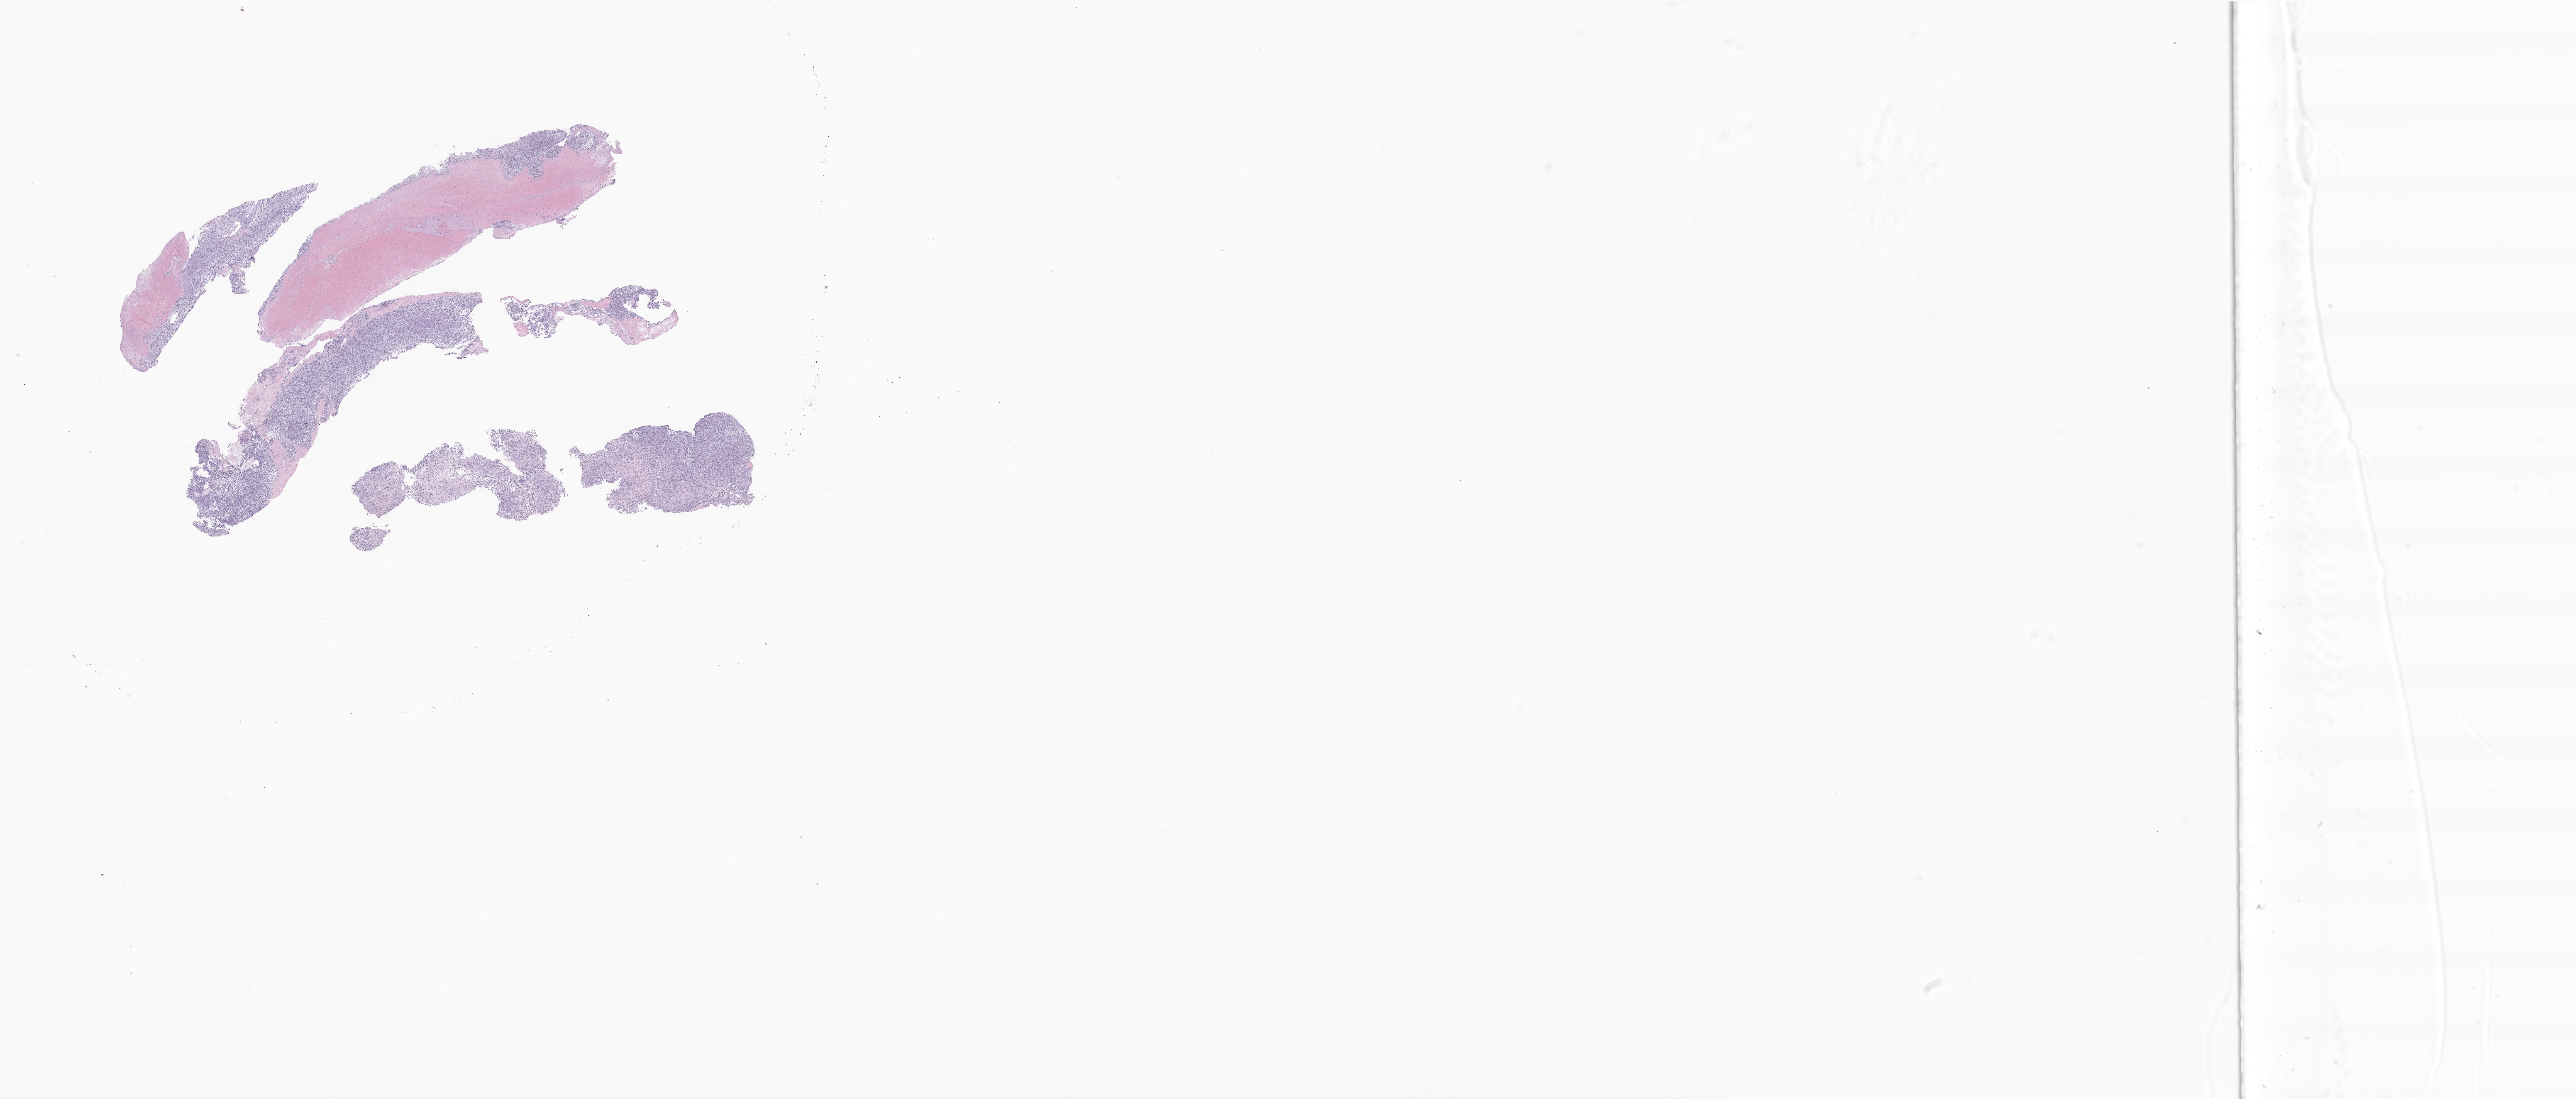
Whole-slide image, H&E stain of tumor tissue from the soft tissue of pelvis, low-resolution overview of the scanned area, about 39.0 x 16.6 mm, formalin-fixed paraffin-embedded section. Patient female; age 89 months (7 years 5 months).
Diagnosis (ICD-O-3 morphology term): Embryonal rhabdomyosarcoma, NOS.